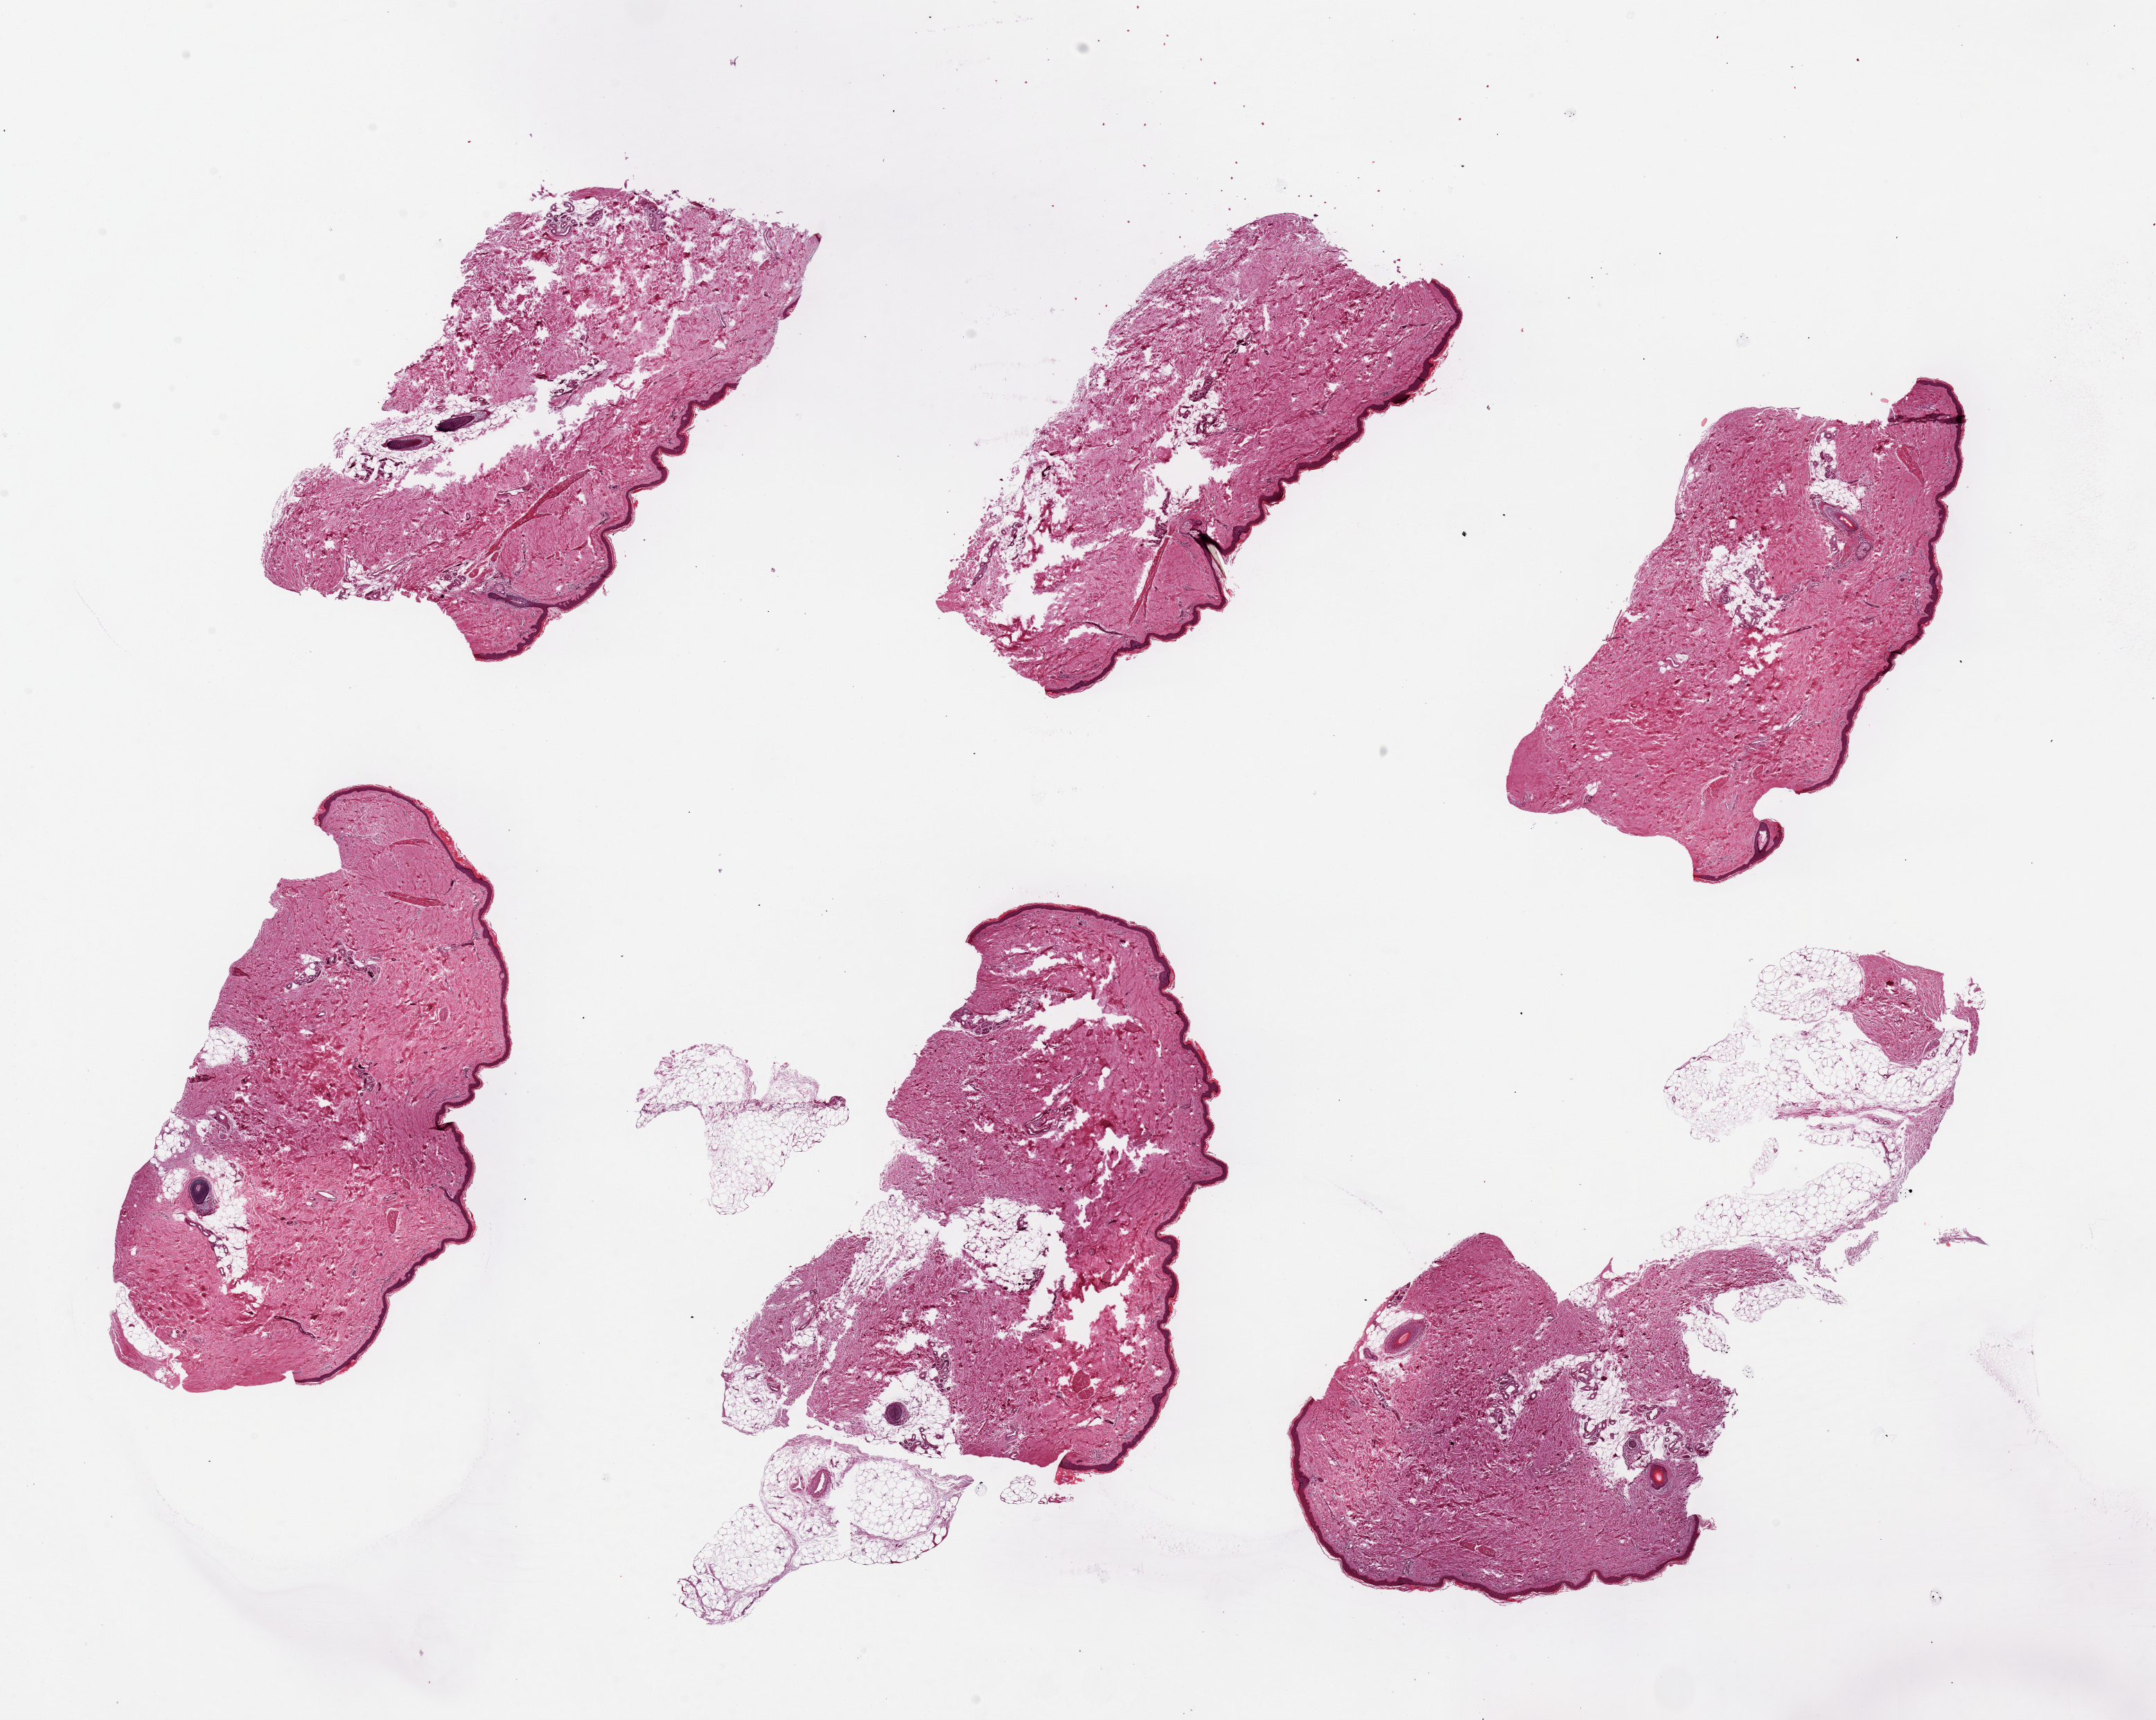
Whole-slide image, hematoxylin and eosin (H&E) stain, brightfield, shown as a low-resolution overview of the whole scanned area (about 24.6 x 19.6 mm); PAXgene-fixed paraffin-embedded (PFPE) section; section of skin of lower leg (target tissue); tissue donor sample. Donor: male.
* reviewer comment on this tissue sample: 6 pieces ~7x3mm. Squamous epithelium is ~2-3% of thickness